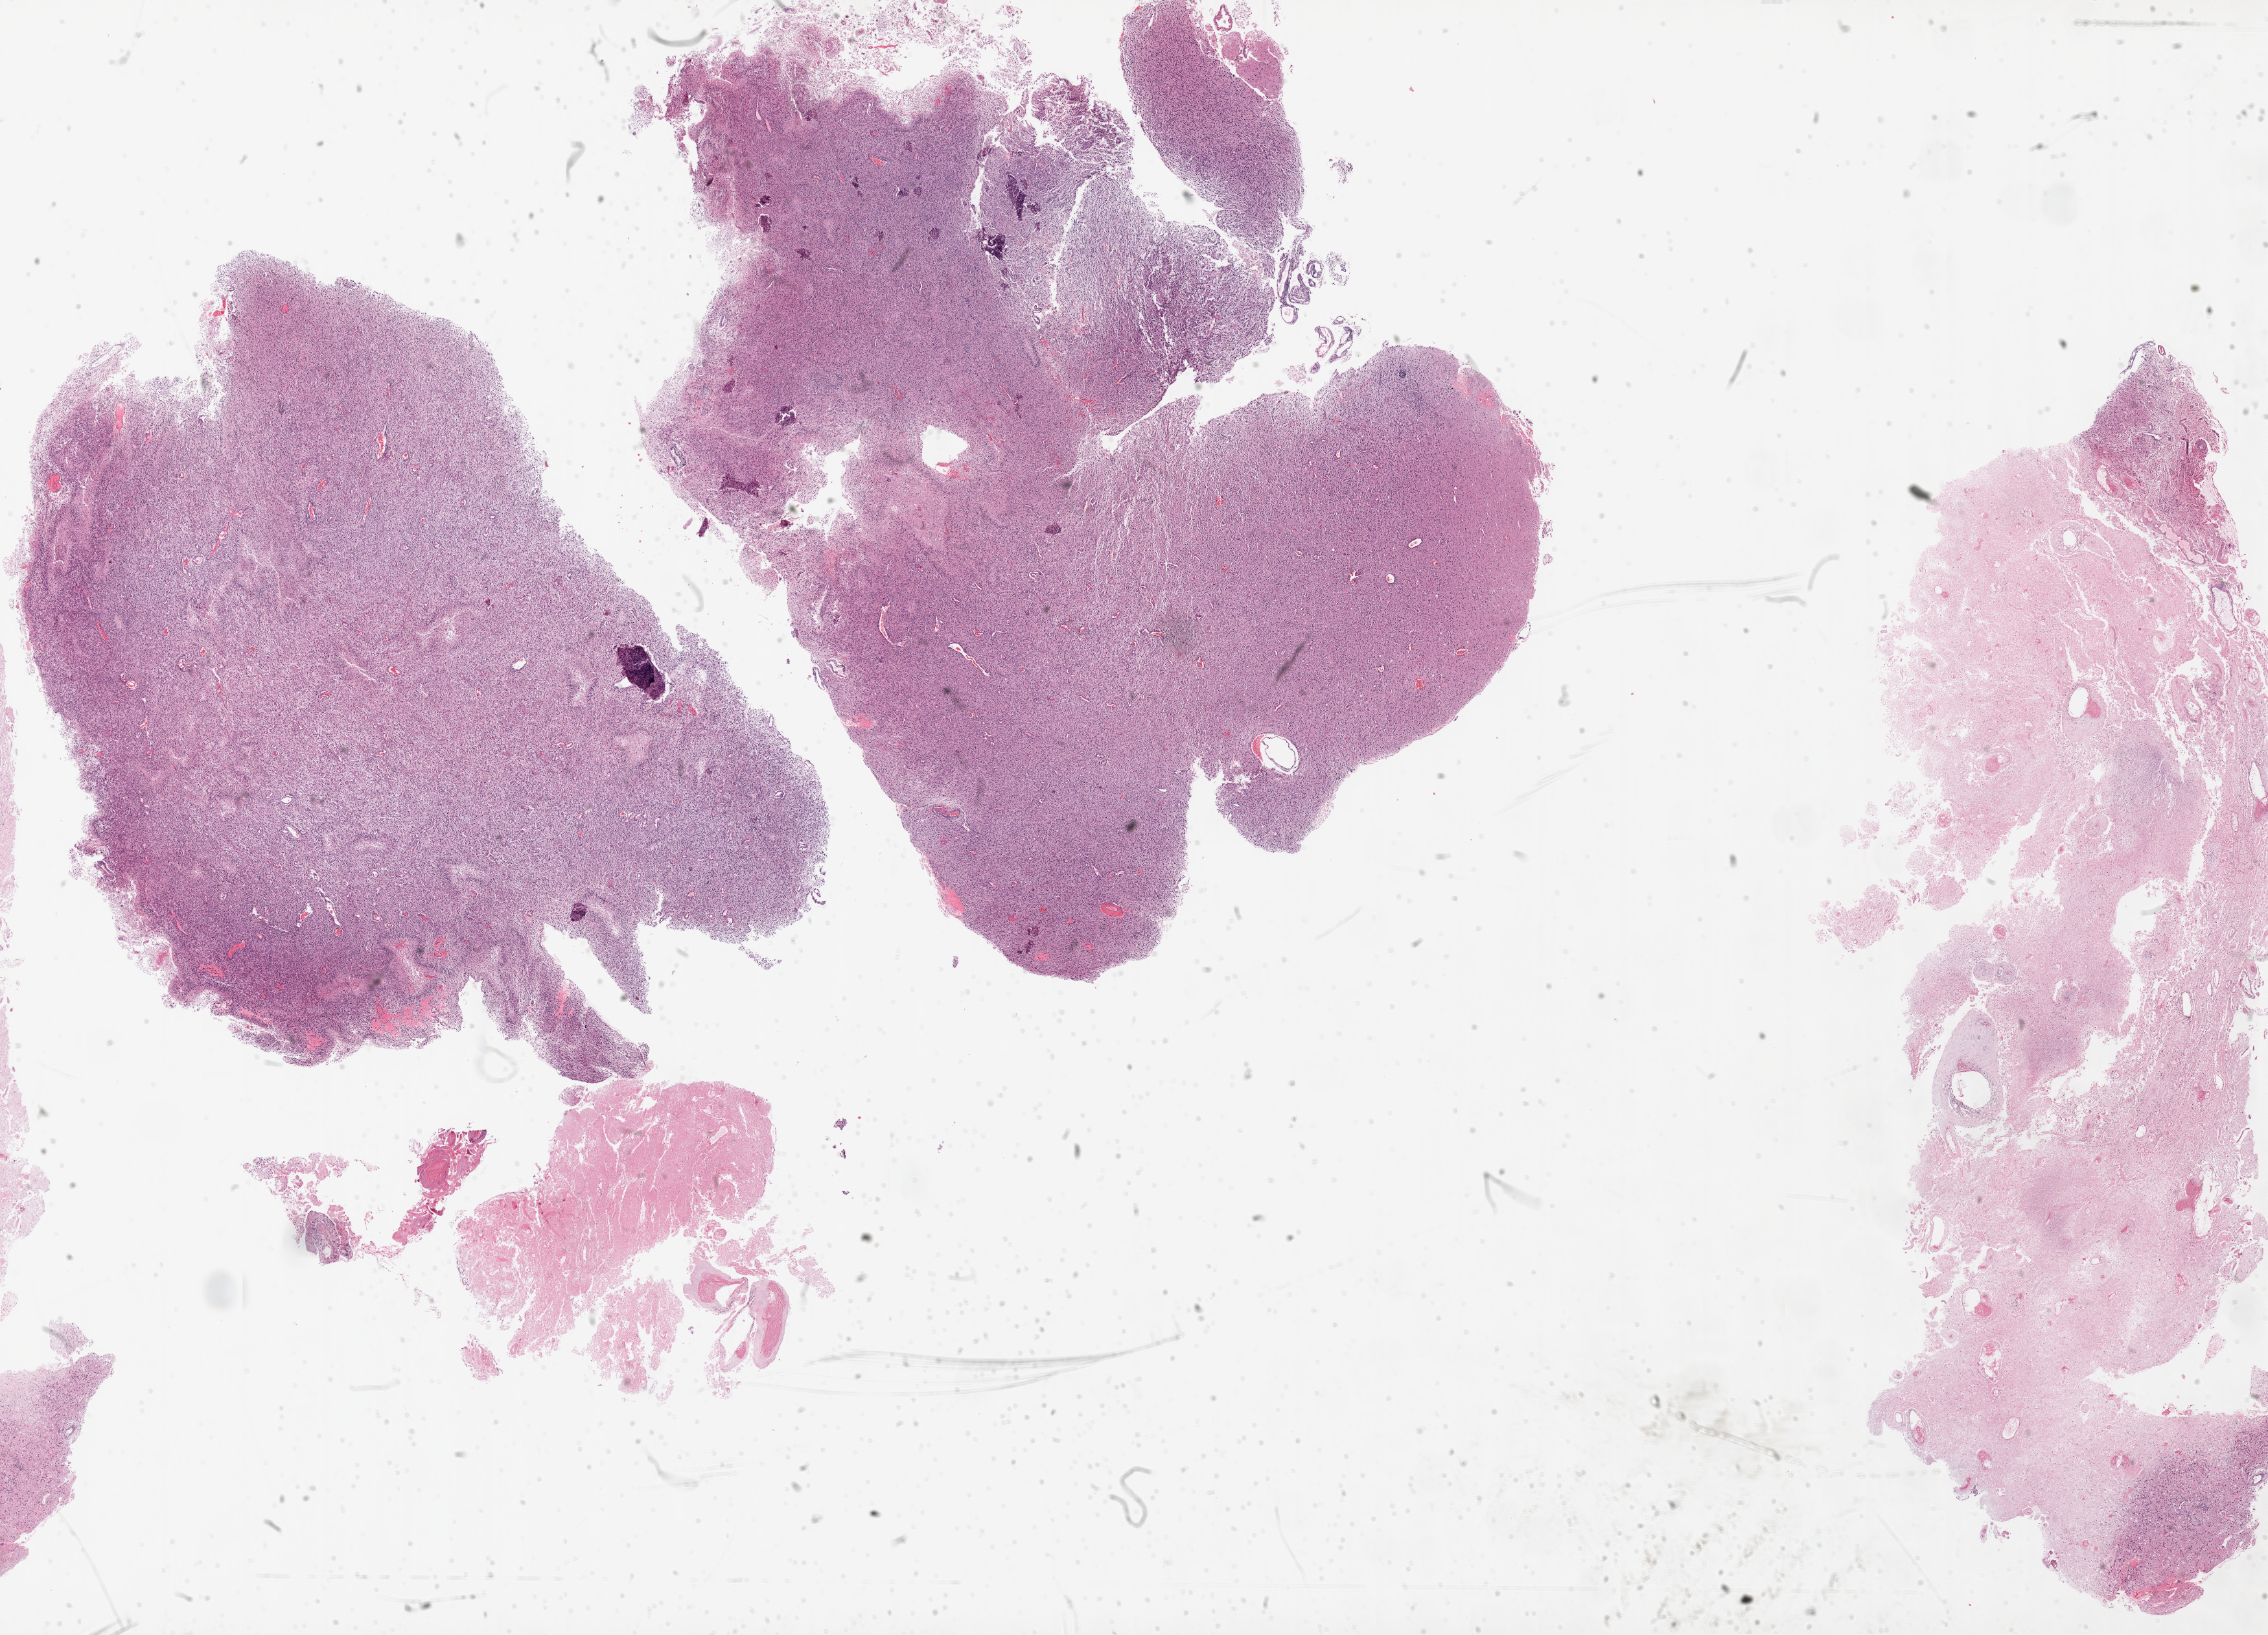
Digitized H&E-stained tissue section (whole slide) — low-resolution overview of the scanned area, about 28.1 x 20.2 mm (from a 20x scan). Formalin-fixed paraffin-embedded (FFPE) diagnostic section. Brain, primary tumour sample. Male, age 60 years at initial diagnosis.
Histologic diagnosis: Glioblastoma.